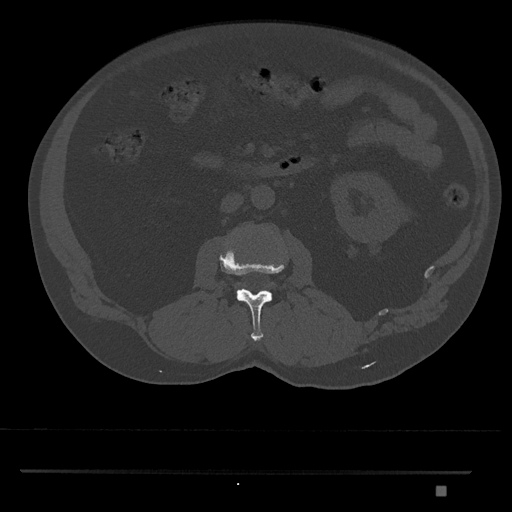
CT including the spine, one axial slice; slice 733 of 1134 in the series (ordered by position); bone window (W 1800 / L 400 HU); 0.5 mm slice thickness; 512 × 512 image matrix. Patient: male, 65 years. From the clinical record (not read from this slice): primary cancer: prostate.
Structures marked on this image (semi-automatic segmentation, software-assisted and operator-edited):
- L2 vertebra: box from (x=219, y=247) to (x=285, y=341) px